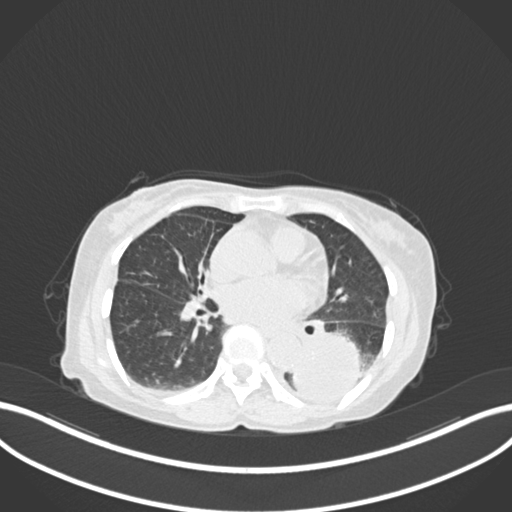
Chest CT, one axial slice. Slice 68 of 233 in the series (ordered by position). Reconstruction kernel B30f. 120 kVp. Lung window (W 1500 / L -600 HU). 1 mm slice thickness. 512 × 512 image matrix, field of view 400 × 400 mm. Female patient, age 78 years. Case-level facts recorded for this patient, not image findings: clinical TNM (as recorded): T3 N0 M1.
Outlined on this slice (bounding box drawn by a radiologist):
- lung tumour (recorded histology: squamous cell carcinoma): bounding box [x1, y1, x2, y2] px = [290, 332, 365, 407]